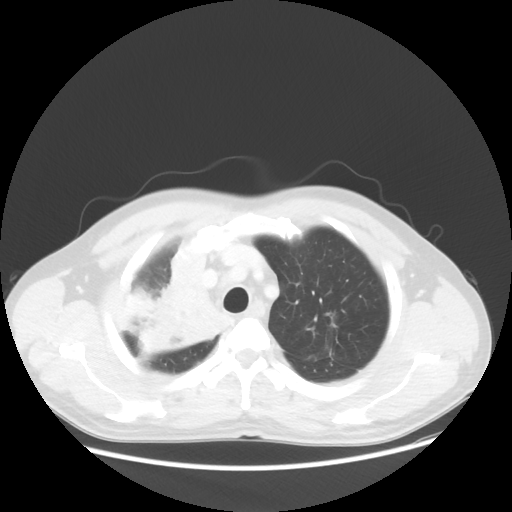
Chest CT, one axial slice. 100 kVp. Lung window (W 1500 / L -600 HU). 5 mm slice thickness. 512 × 512 image matrix, field of view 398 × 398 mm. Male patient, age 60 years. Case-level facts recorded for this patient, not image findings: clinical TNM (as recorded): T2a N1 M0.
Structures marked on this image (rectangle marked by the reading radiologist):
- lung tumour (recorded histology: squamous cell carcinoma): bounding box [x1, y1, x2, y2] px = [118, 241, 228, 362]